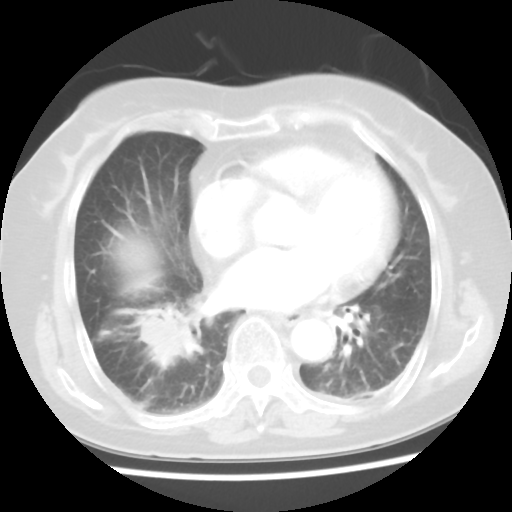
Chest CT, one axial slice. Slice 18 of 45 in the series (ordered by position). Lung window (W 1500 / L -600 HU). 5 mm slice thickness. 512 × 512 image matrix, field of view 312 × 312 mm. Patient: female, 65 years. Case-level facts recorded for this patient, not image findings: clinical TNM (as recorded): T2 N3 M0.
Outlined on this slice (rectangle marked by the reading radiologist):
- lung tumour (recorded histology: adenocarcinoma): bounding box <131,303,213,375> (left, top, right, bottom; pixels)